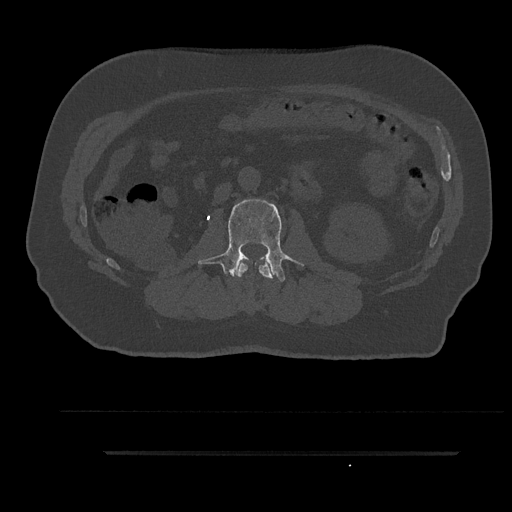
CT including the spine, one axial slice; position 121 of 797 along the scan axis; reconstruction kernel Br40s/3; 120 kVp; bone window (W 1800 / L 400 HU); 0.5 mm slice thickness; 512 × 512 image matrix, field of view 432 × 432 mm. Male patient, age 63 years. Case-level facts recorded for this patient, not image findings: primary cancer: renal.
Outlined on this slice (semi-automatically segmented with operator editing):
- L1 vertebra: bounding box <237,259,274,279> (left, top, right, bottom; pixels)
- L2 vertebra: <198,199,304,282>